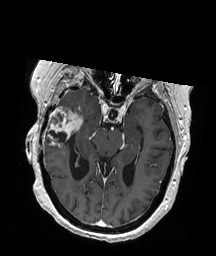
Brain MRI from a brain-tumour surgery series, one axial slice. Position 118 of 192 along the scan axis. T1-weighted post-contrast. 1 mm slice thickness. 216 × 256 image matrix, field of view 211 × 250 mm. Case-level facts recorded for this patient, not image findings: histopathology: Glioblastoma; WHO grade: 4; IDH mutation: no; tumour location: Right Temporal.
Structures marked on this image (outlined manually by an expert reader):
- tumour: box from (x=47, y=108) to (x=83, y=146) px